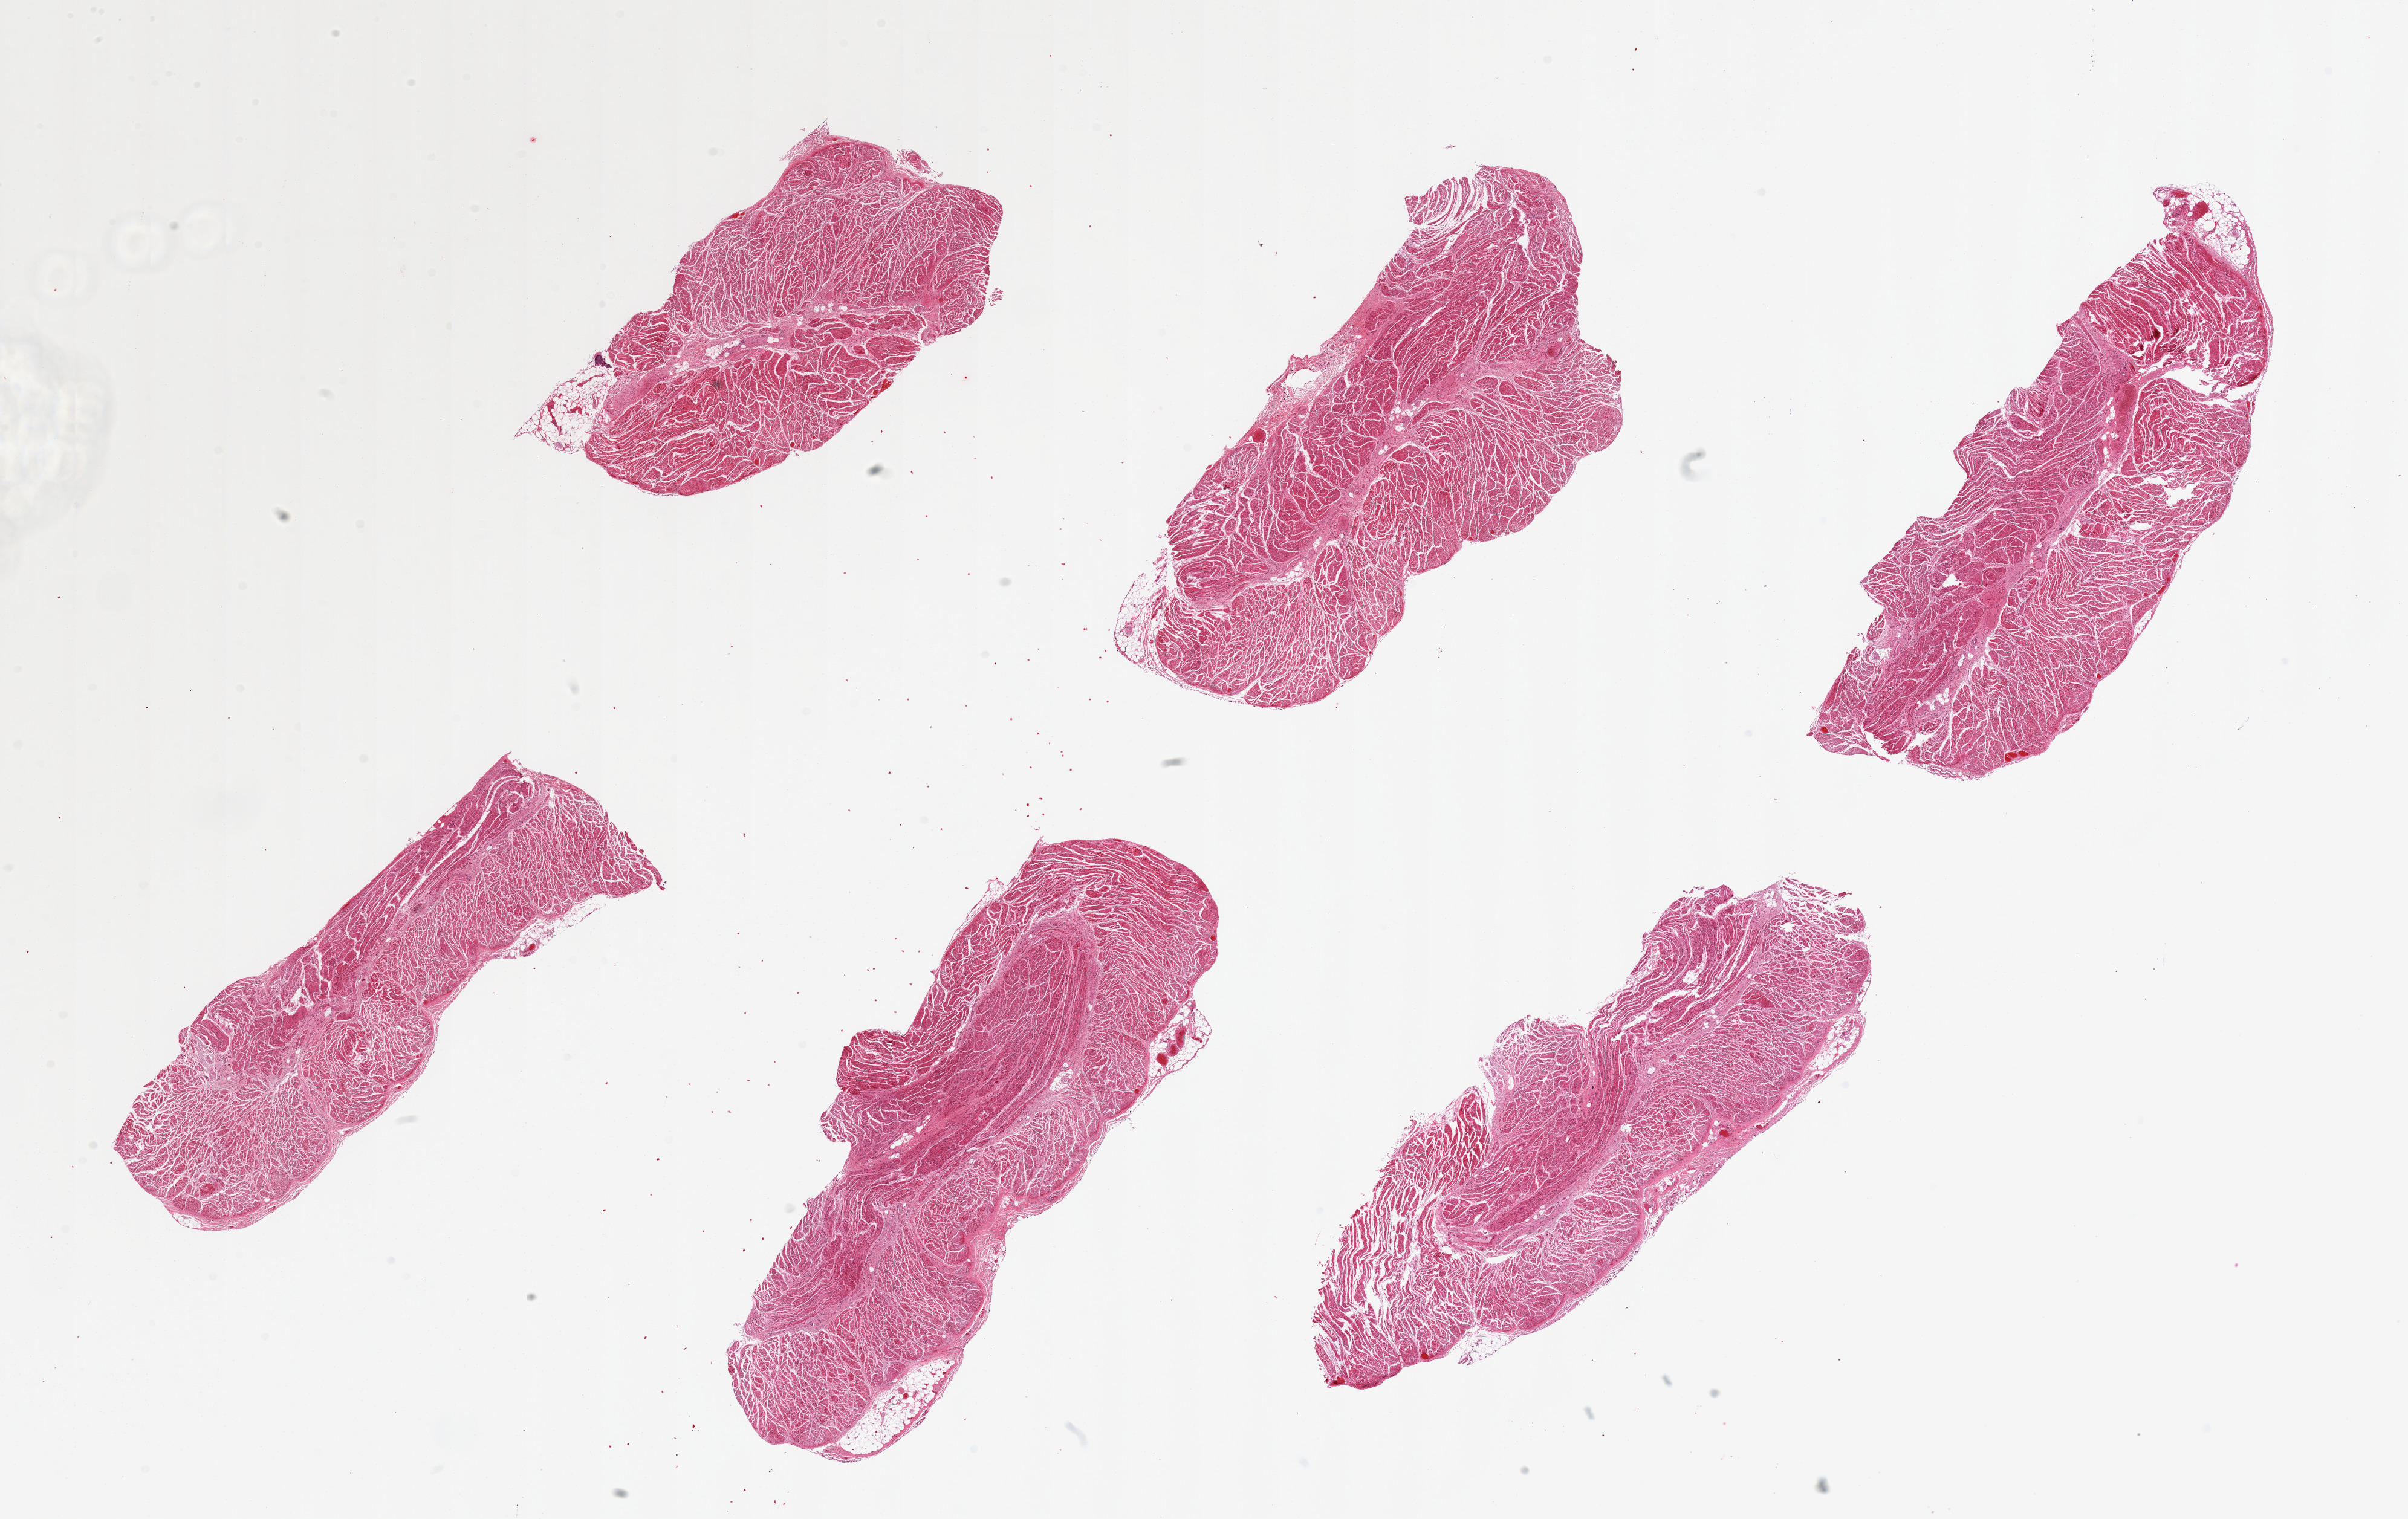
Haematoxylin and eosin whole-slide image, whole scanned area (about 31.5 x 19.9 mm) shown as a low-resolution overview; PAXgene-fixed, paraffin-embedded tissue; target tissue: gastroesophageal junction; tissue donor sample. Donor: male.
Review note (as recorded): 6 pieces, all muscularis, good specimens.